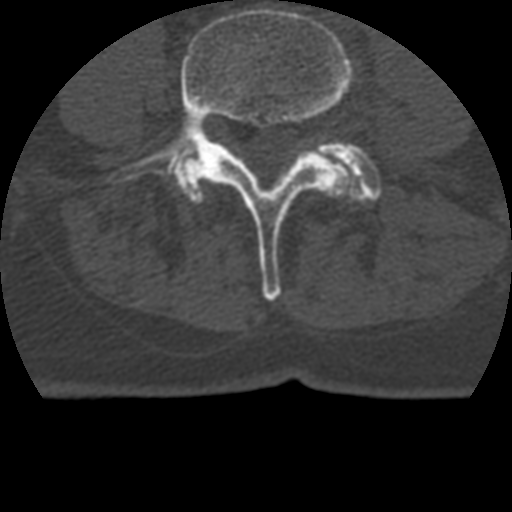
CT including the spine, one axial slice. Slice 62 of 399 in the series (ordered by position). Reconstruction kernel STANDARD. Bone window (W 1800 / L 400 HU). 1.25 mm slice thickness. 512 × 512 image matrix, field of view 160 × 160 mm. Patient age 69 years. From the clinical record (not read from this slice): primary cancer: prostate.
Structures marked on this image (semi-automatically segmented with operator editing):
- L4 vertebra: bounding box <108,8,352,301> (left, top, right, bottom; pixels)
- L5 vertebra: <177,141,382,202>